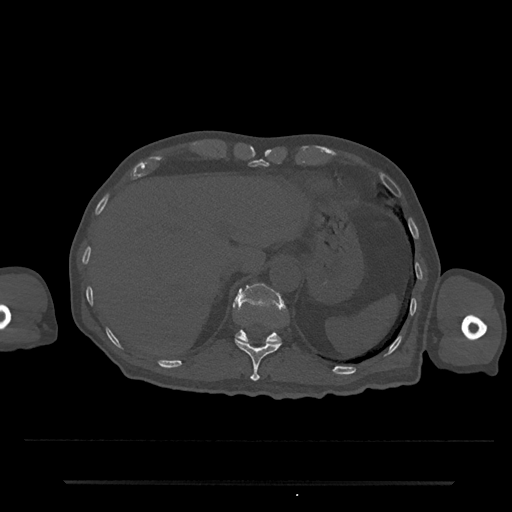
CT including the spine, one axial slice. Slice 234 of 797 in the series (ordered by position). Reconstruction kernel Br40s/3. 120 kVp. Bone window (W 1800 / L 400 HU). 512 × 512 image matrix, field of view 427 × 427 mm. Male patient, age 74 years. From the clinical record (not read from this slice): primary cancer: prostate.
Annotated regions visible in this slice (semi-automatic segmentation, software-assisted and operator-edited):
- T11 vertebra: bounding box [x1, y1, x2, y2] px = [234, 338, 282, 382]
- T12 vertebra: [236, 283, 282, 344]